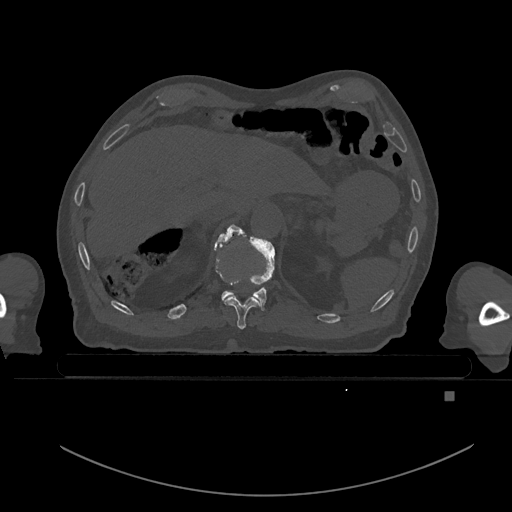
CT including the spine, one axial slice. Slice 61 of 969 in the series (ordered by position). Bone window (W 1800 / L 400 HU). 512 × 512 image matrix. Patient: male, 82 years. From the clinical record (not read from this slice): primary cancer: prostate; vertebrae with lytic lesions (as recorded): T11, T9, T8, T2.
Outlined on this slice (semi-automatic segmentation, software-assisted and operator-edited):
- T10 vertebra: box from (x=214, y=240) to (x=260, y=330) px
- T11 vertebra: (x=218, y=224)–(x=275, y=309)